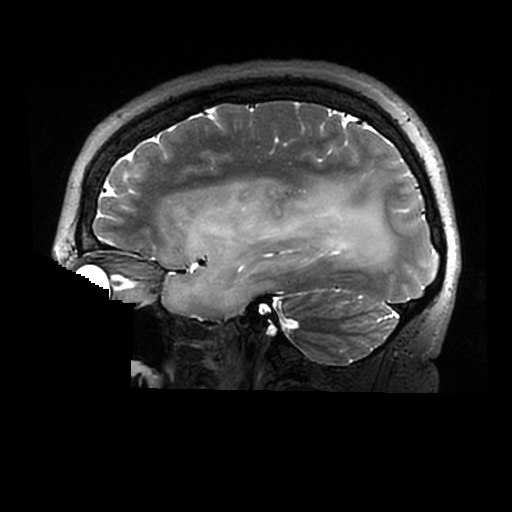
Brain MRI from a brain-tumour surgery series, one sagittal slice. Slice 203 of 320 in the series (ordered by position). 512 × 512 image matrix, field of view 240 × 240 mm. From the clinical record (not read from this slice): histopathology: Astrocytoma; WHO grade: 2; IDH mutation: yes.
Outlined on this slice (manually delineated by an expert):
- tumour: bounding box [x1, y1, x2, y2] px = [162, 180, 395, 317]